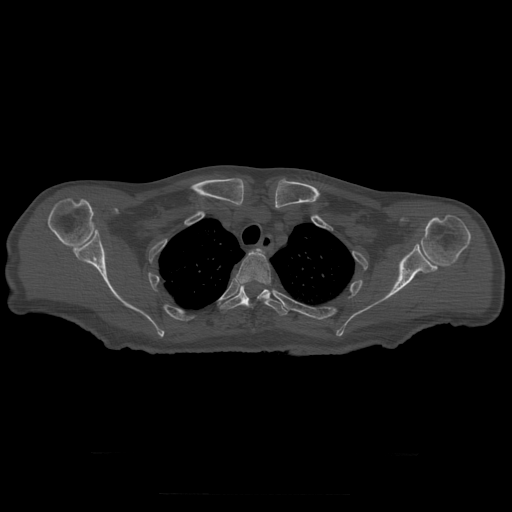
CT including the spine, one axial slice. Slice 251 of 397 in the series (ordered by position). Bone window (W 1800 / L 400 HU). 1.25 mm slice thickness. 512 × 512 image matrix, field of view 510 × 510 mm. Patient age 73 years. Case-level facts recorded for this patient, not image findings: primary cancer: prostate.
Outlined on this slice (semi-automatic segmentation, software-assisted and operator-edited):
- T2 vertebra: bounding box [x1, y1, x2, y2] px = [256, 249, 264, 253]
- T3 vertebra: [236, 251, 271, 293]
- T4 vertebra: [220, 286, 288, 316]